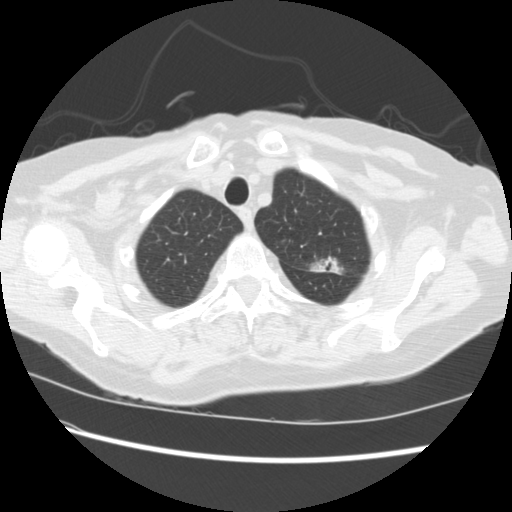
Low-dose screening chest CT, one axial slice. Position 188 of 224 along the scan axis. Reconstruction kernel STANDARD. Lung window (W 1500 / L -600 HU). 2.5 mm slice thickness. 512 × 512 image matrix.
Structures marked on this image (expert manual segmentation):
- lesion 1 (tumor, upper lobe of left lung): box from (x=311, y=257) to (x=341, y=274) px